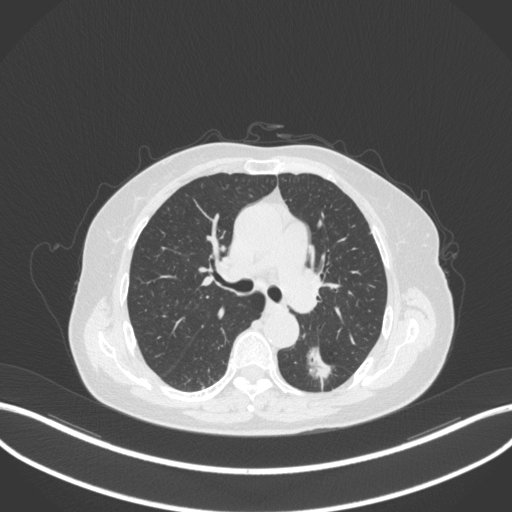
Chest CT, one axial slice; position 186 of 352 along the scan axis; reconstruction kernel B31f; lung window (W 1500 / L -600 HU); 1 mm slice thickness; 512 × 512 image matrix, field of view 400 × 400 mm. Female patient, age 70 years. From the clinical record (not read from this slice): clinical TNM (as recorded): T1c N0 M0.
Annotated regions visible in this slice (bounding box drawn by a radiologist):
- lung tumour (recorded histology: adenocarcinoma): bounding box (x1, y1, x2, y2) in pixels: (301, 335, 334, 385)